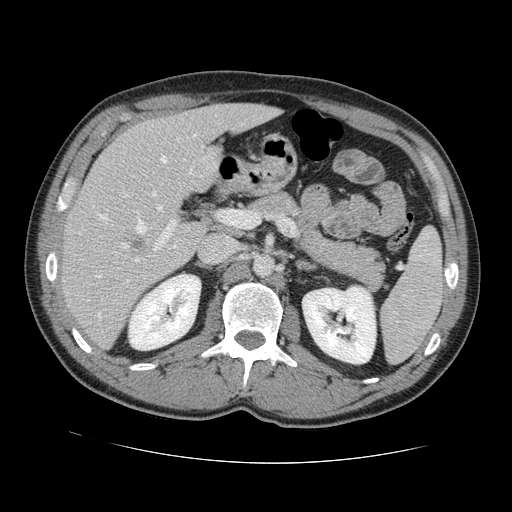
Contrast-enhanced abdominal CT, one axial slice. Slice 76 of 131 in the series (ordered by position). Intravenous contrast given. Soft-tissue window (W 400 / L 40 HU). 2.5 mm slice thickness. 512 × 512 image matrix, field of view 380 × 380 mm. Male patient, age 40 years. From the clinical record (not read from this slice): diagnosis: colorectal cancer liver metastases, imaged before liver resection; multiple liver metastases: yes.
Outlined on this slice (manually delineated by an expert):
- hepatic veins: box from (x=96, y=155) to (x=168, y=317) px
- liver: (x=64, y=105)–(x=275, y=346)
- planned liver remnant (the part of the liver to remain after resection): (x=106, y=105)–(x=275, y=197)
- portal vein (with intrahepatic branches): (x=134, y=191)–(x=234, y=262)
- liver metastasis: (x=130, y=235)–(x=148, y=251)